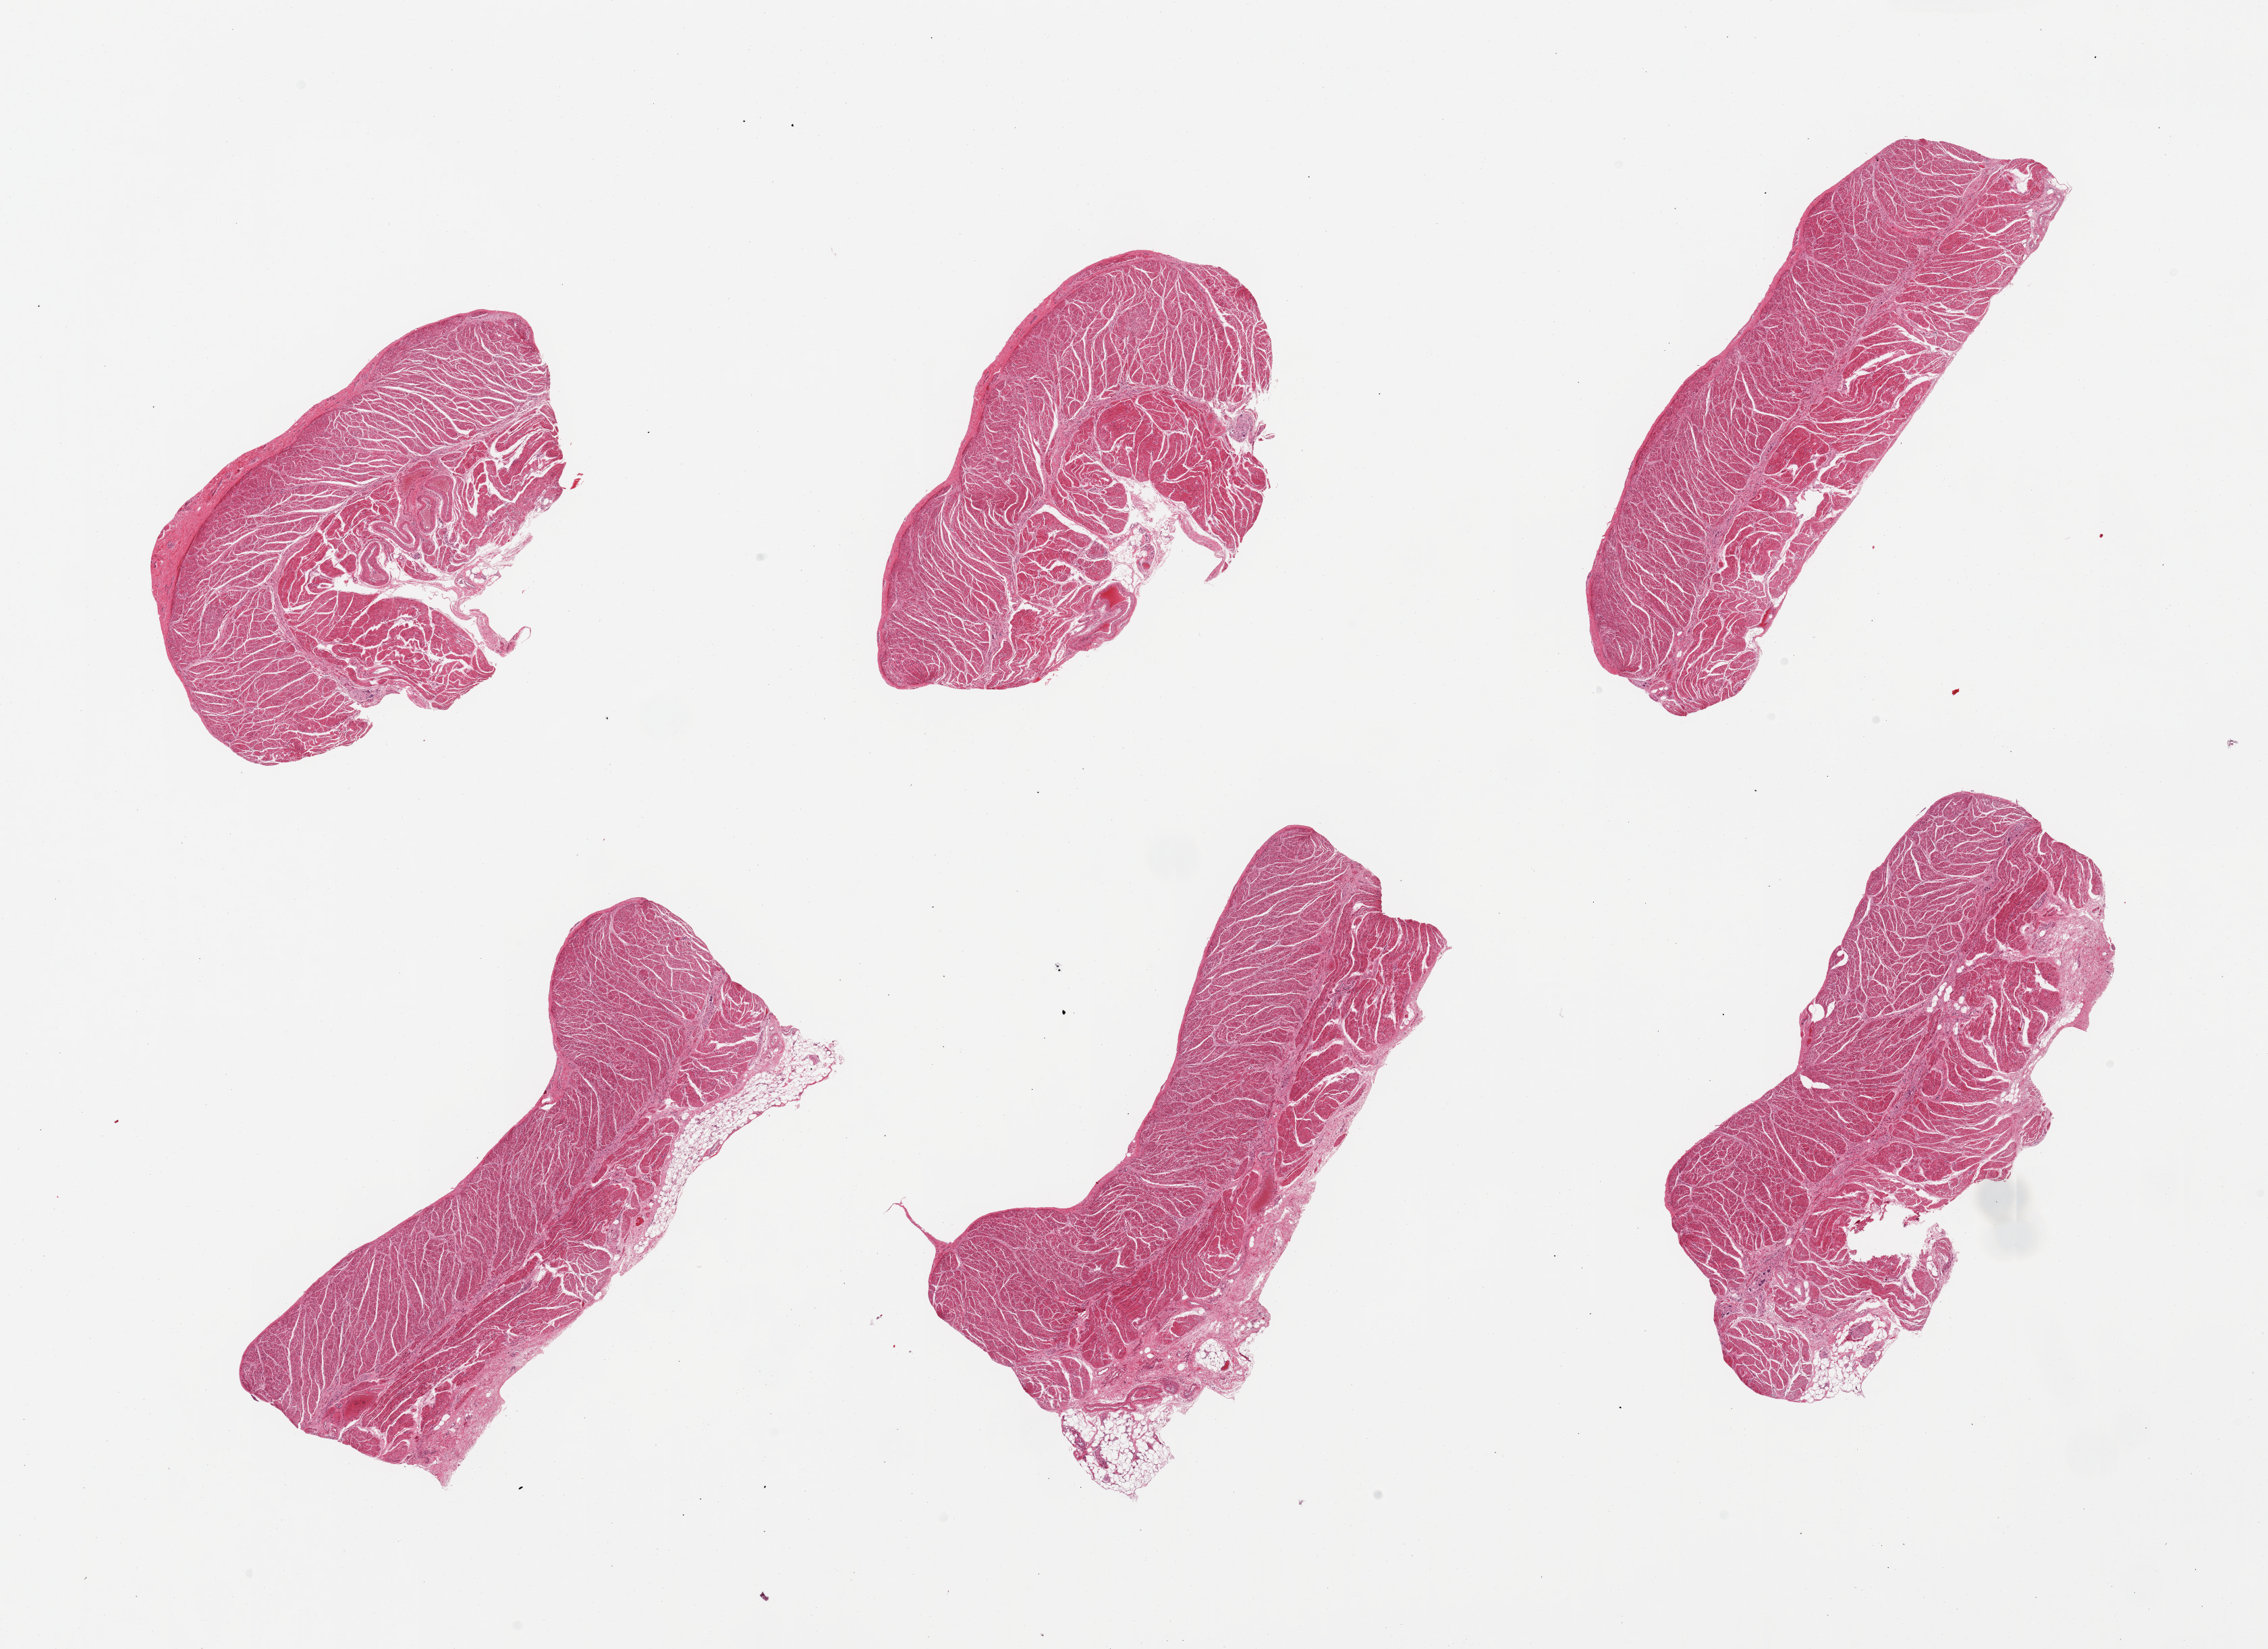
Hematoxylin and eosin (H&E) whole-slide image, brightfield, low-resolution overview of the scanned area, about 26.6 x 19.3 mm (from a 20x scan), PAXgene-fixed paraffin-embedded (PFPE) section, target tissue: gastroesophageal junction, tissue donor sample. Male donor.
Reviewer comment on this tissue sample: 6 pieces; well trimmed, small attachment of fat.